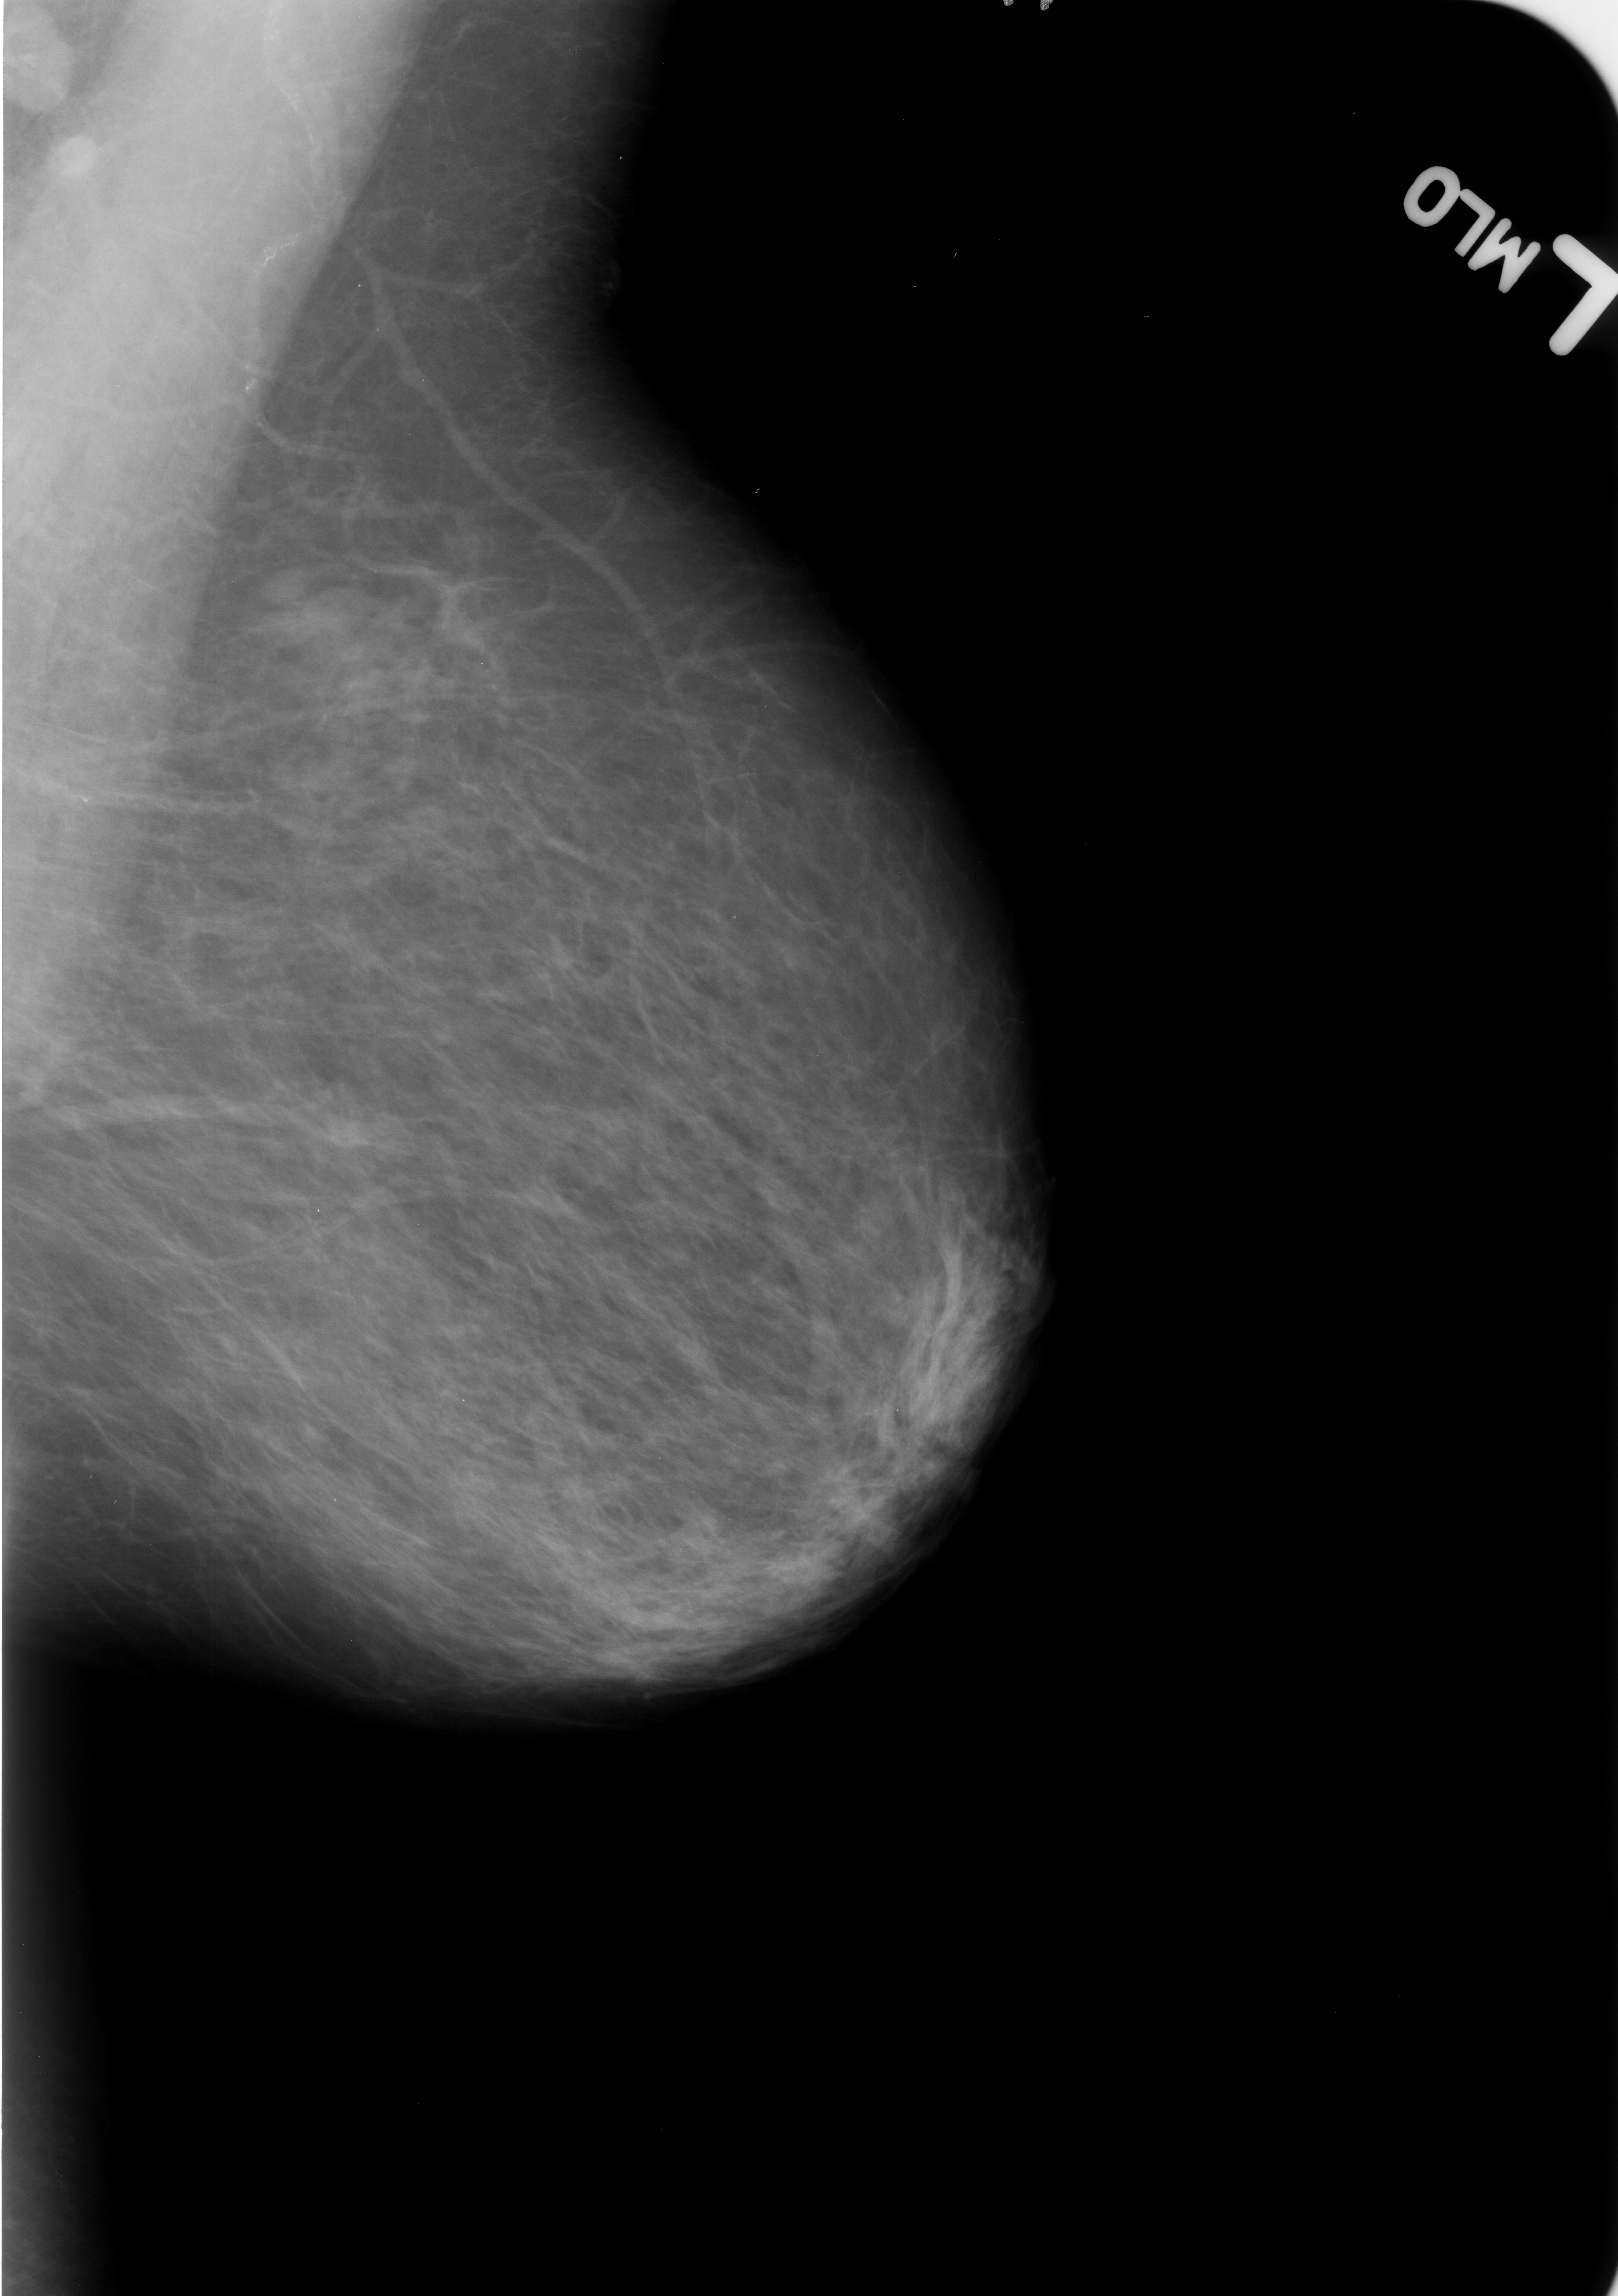
Mammogram (digitized film); left breast; MLO view.
Finding: calcifications, morphology vascular; BI-RADS assessment category 2; benign; no additional work-up was recommended (benign without callback).